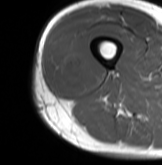
MRI of an extremity soft-tissue mass, one axial slice. Slice 24 of 61 in the series (ordered by position). MR volume resampled by the dataset authors to the PET/CT grid (not the native acquisition matrix). 3.27 mm slice thickness. 162 × 165 image matrix, field of view 158 × 161 mm. Male patient. Case-level facts recorded for this patient, not image findings: histological type: poorly differentiated synovial sarcoma; grade: high; site of the primary tumour: right buttock.
Annotated regions visible in this slice (expert contour drawn on MRI and transferred to this co-registered scan by the dataset authors):
- gross tumour volume including surrounding oedema: bounding box [x1, y1, x2, y2] px = [50, 40, 101, 96]
- gross tumour volume (mass): [52, 43, 88, 92]